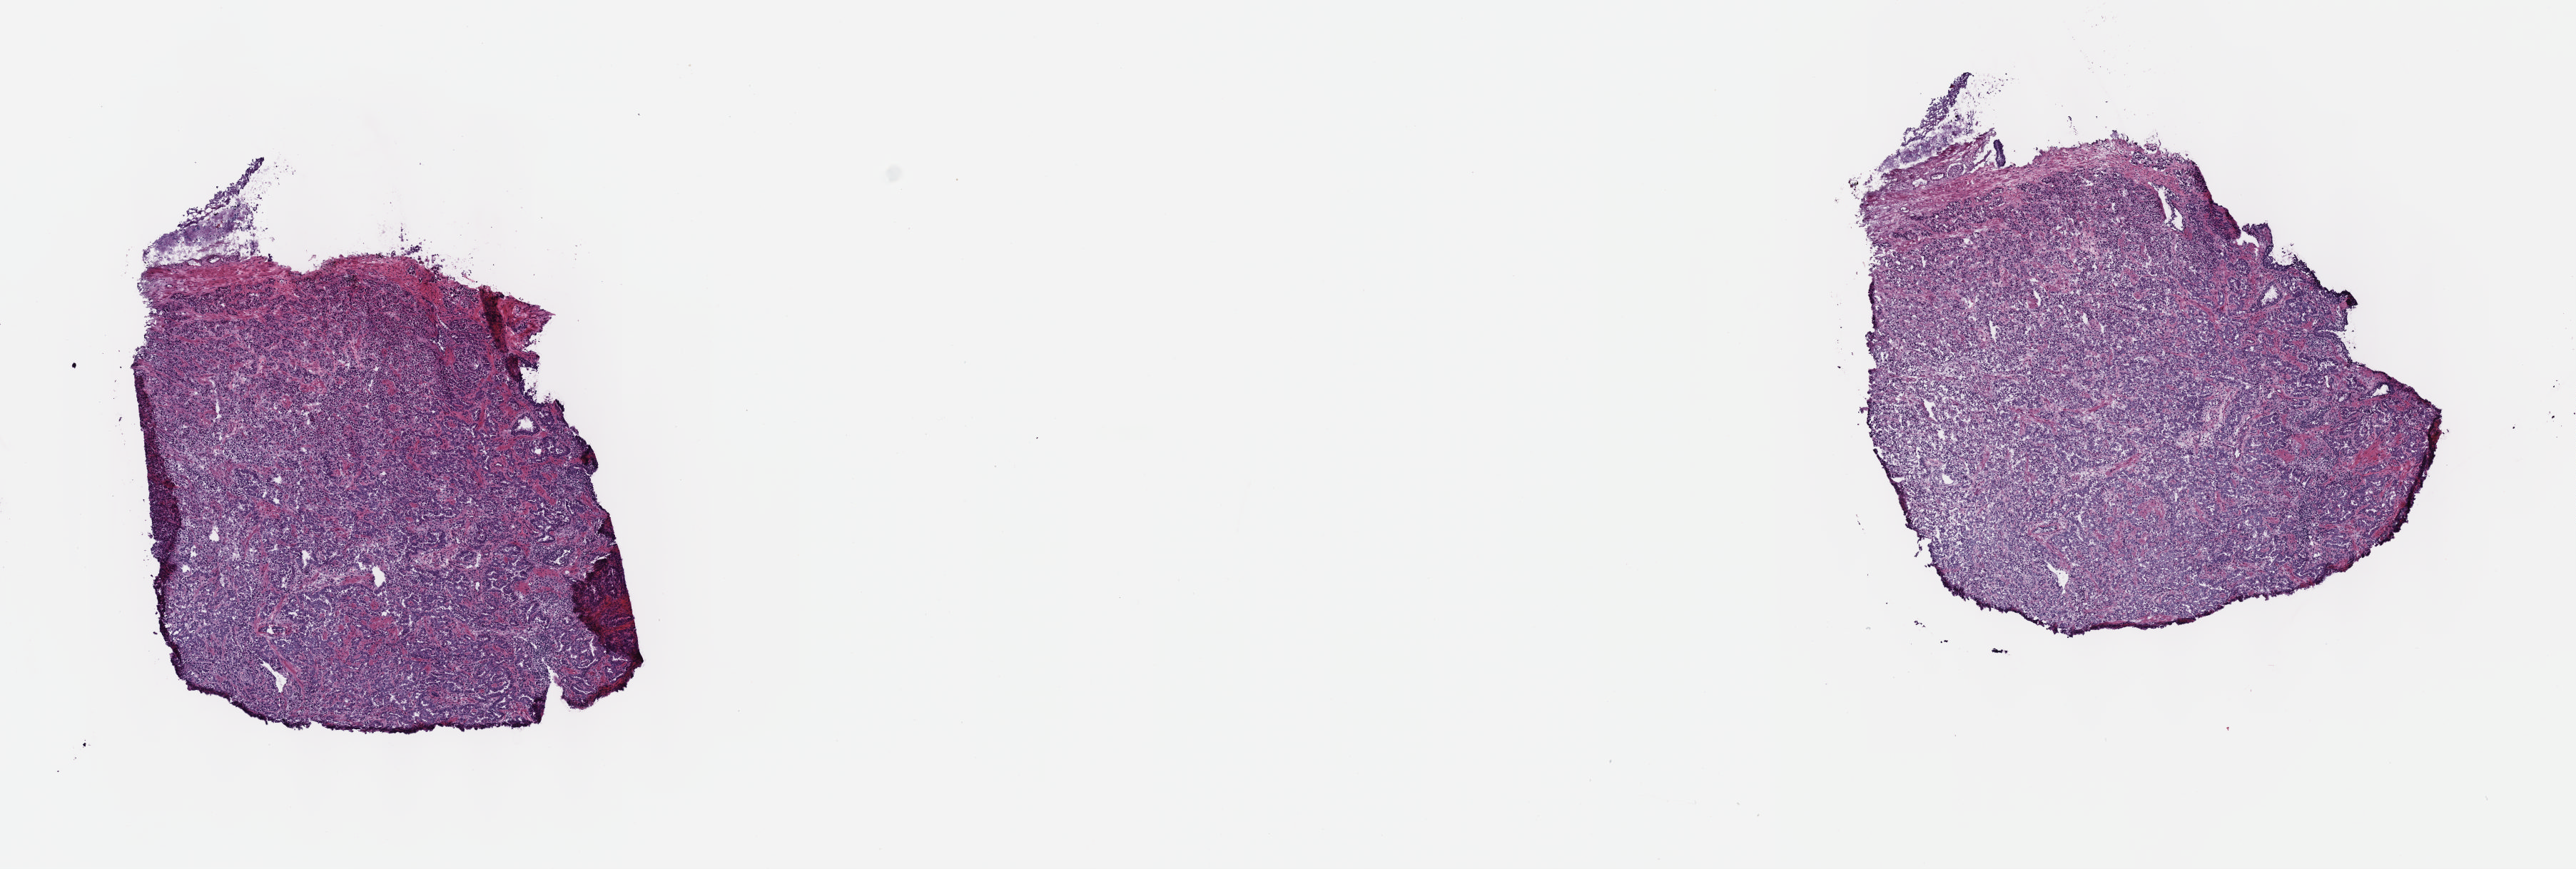
Digitized Hematoxylin and eosin (H&E) stained tissue section (whole slide), whole scanned area (about 14.6 x 4.9 mm, acquisition: 40x scan) shown as a low-resolution overview; frozen section from the top of the tissue portion; primary tumour sample from the prostate. Male, age 68 years at initial diagnosis. Gleason score: 7 (3+4). Pathologist review of this section (percent, as recorded): tumour cells 90%, tumour nuclei 90%, normal cells 0%, stromal cells 10%, necrosis 0%. Infiltration values recorded for this section: lymphocyte infiltration 0%, monocyte infiltration 0%, neutrophil infiltration 0%.
Lymph nodes positive (case pathology): 0 of 1 examined. Histologic diagnosis: Adenocarcinoma, NOS (prostate gland).